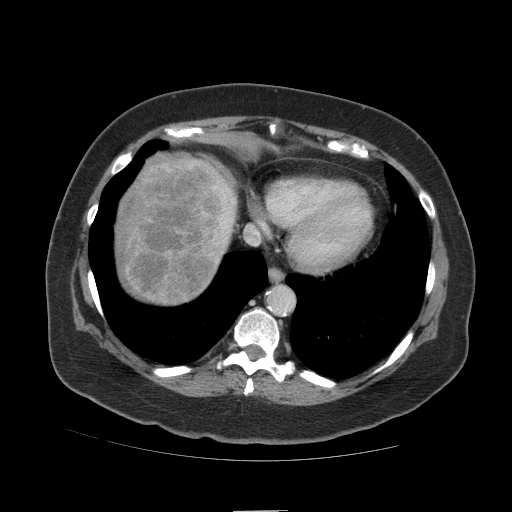
Contrast-enhanced abdominal CT (liver protocol), one axial slice; position 96 of 109 along the scan axis; reconstruction kernel STANDARD; 140 kVp; soft-tissue window (W 400 / L 40 HU); 512 × 512 image matrix, field of view 420 × 420 mm. From the clinical record (not read from this slice): diagnosis: hepatocellular carcinoma (patient treated with transarterial chemoembolisation; whether this scan precedes or follows treatment is not stated here); TNM stage (as recorded): Stage-IVB; Child-Pugh class: A.
Outlined on this slice (semi-automatic segmentation, software-assisted and operator-edited):
- liver parenchyma outside the tumour (the mass and vessels are separate outlines, so this box may not span the whole liver): bounding box (x1, y1, x2, y2) in pixels: (116, 154, 236, 304)
- mass: (117, 157, 234, 300)